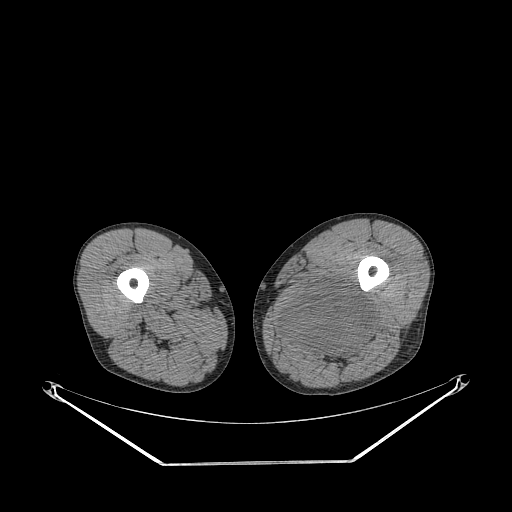
CT of an extremity soft-tissue mass (from a PET/CT study), one axial slice; reconstruction kernel STANDARD; soft-tissue window (W 400 / L 40 HU); 3.75 mm slice thickness; 512 × 512 image matrix, field of view 500 × 500 mm. Male patient. Case-level facts recorded for this patient, not image findings: histological type: undifferentiated pleomorphic liposarcoma; grade: high; site of the primary tumour: left thigh.
Outlined on this slice (expert contour drawn on MRI and transferred to this co-registered scan by the dataset authors):
- gross tumour volume including surrounding oedema: box from (x=276, y=285) to (x=375, y=362) px
- gross tumour volume (mass): (x=281, y=285)–(x=375, y=353)